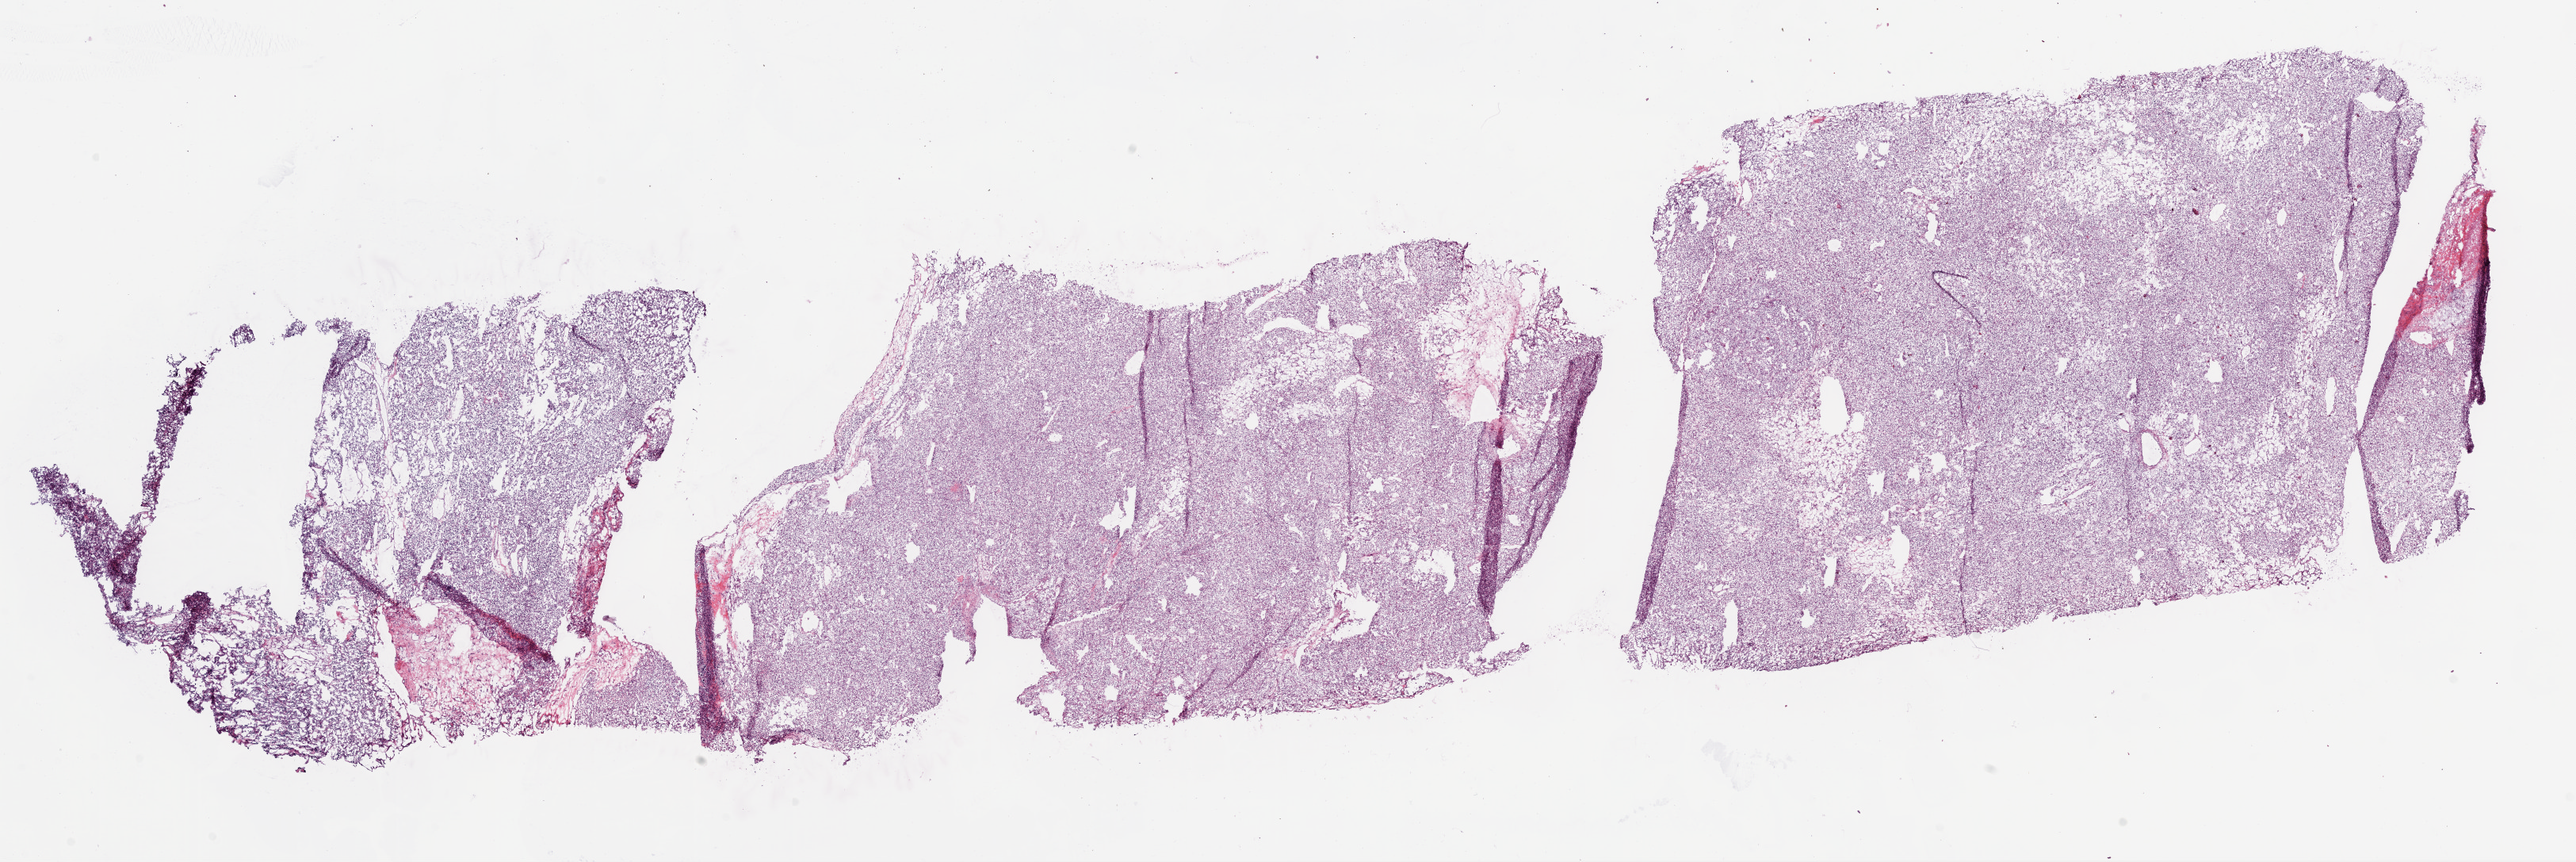
Digitized H&E tissue section (whole slide) — shown as a low-resolution overview of the whole scanned area (about 26.1 x 8.7 mm, from a 20x scan); frozen section; kidney, primary tumour sample. Patient: female, age at initial diagnosis 62 years. Histologic grade: G2 (moderately differentiated). Composition of this section per pathologist review: tumour cells 90%, tumour nuclei 85%, normal cells 0%, stromal cells 10%, necrosis 0%.
• AJCC pathologic stage: I
• histologic diagnosis: Clear cell adenocarcinoma, NOS
• laterality: right